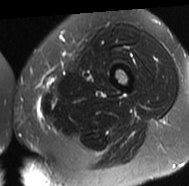
MRI of an extremity soft-tissue mass, one axial slice. Position 13 of 77 along the scan axis. T2-weighted fat-saturated. MR volume resampled by the dataset authors to the PET/CT grid (not the native acquisition matrix). 3.27 mm slice thickness. 189 × 186 image matrix. Female patient. From the clinical record (not read from this slice): histological type: leiomyosarcoma; grade: high; site of the primary tumour: groin.
Annotated regions visible in this slice (expert contour drawn on MRI and transferred to this co-registered scan by the dataset authors):
- gross tumour volume including surrounding oedema: box from (x=17, y=118) to (x=20, y=121) px